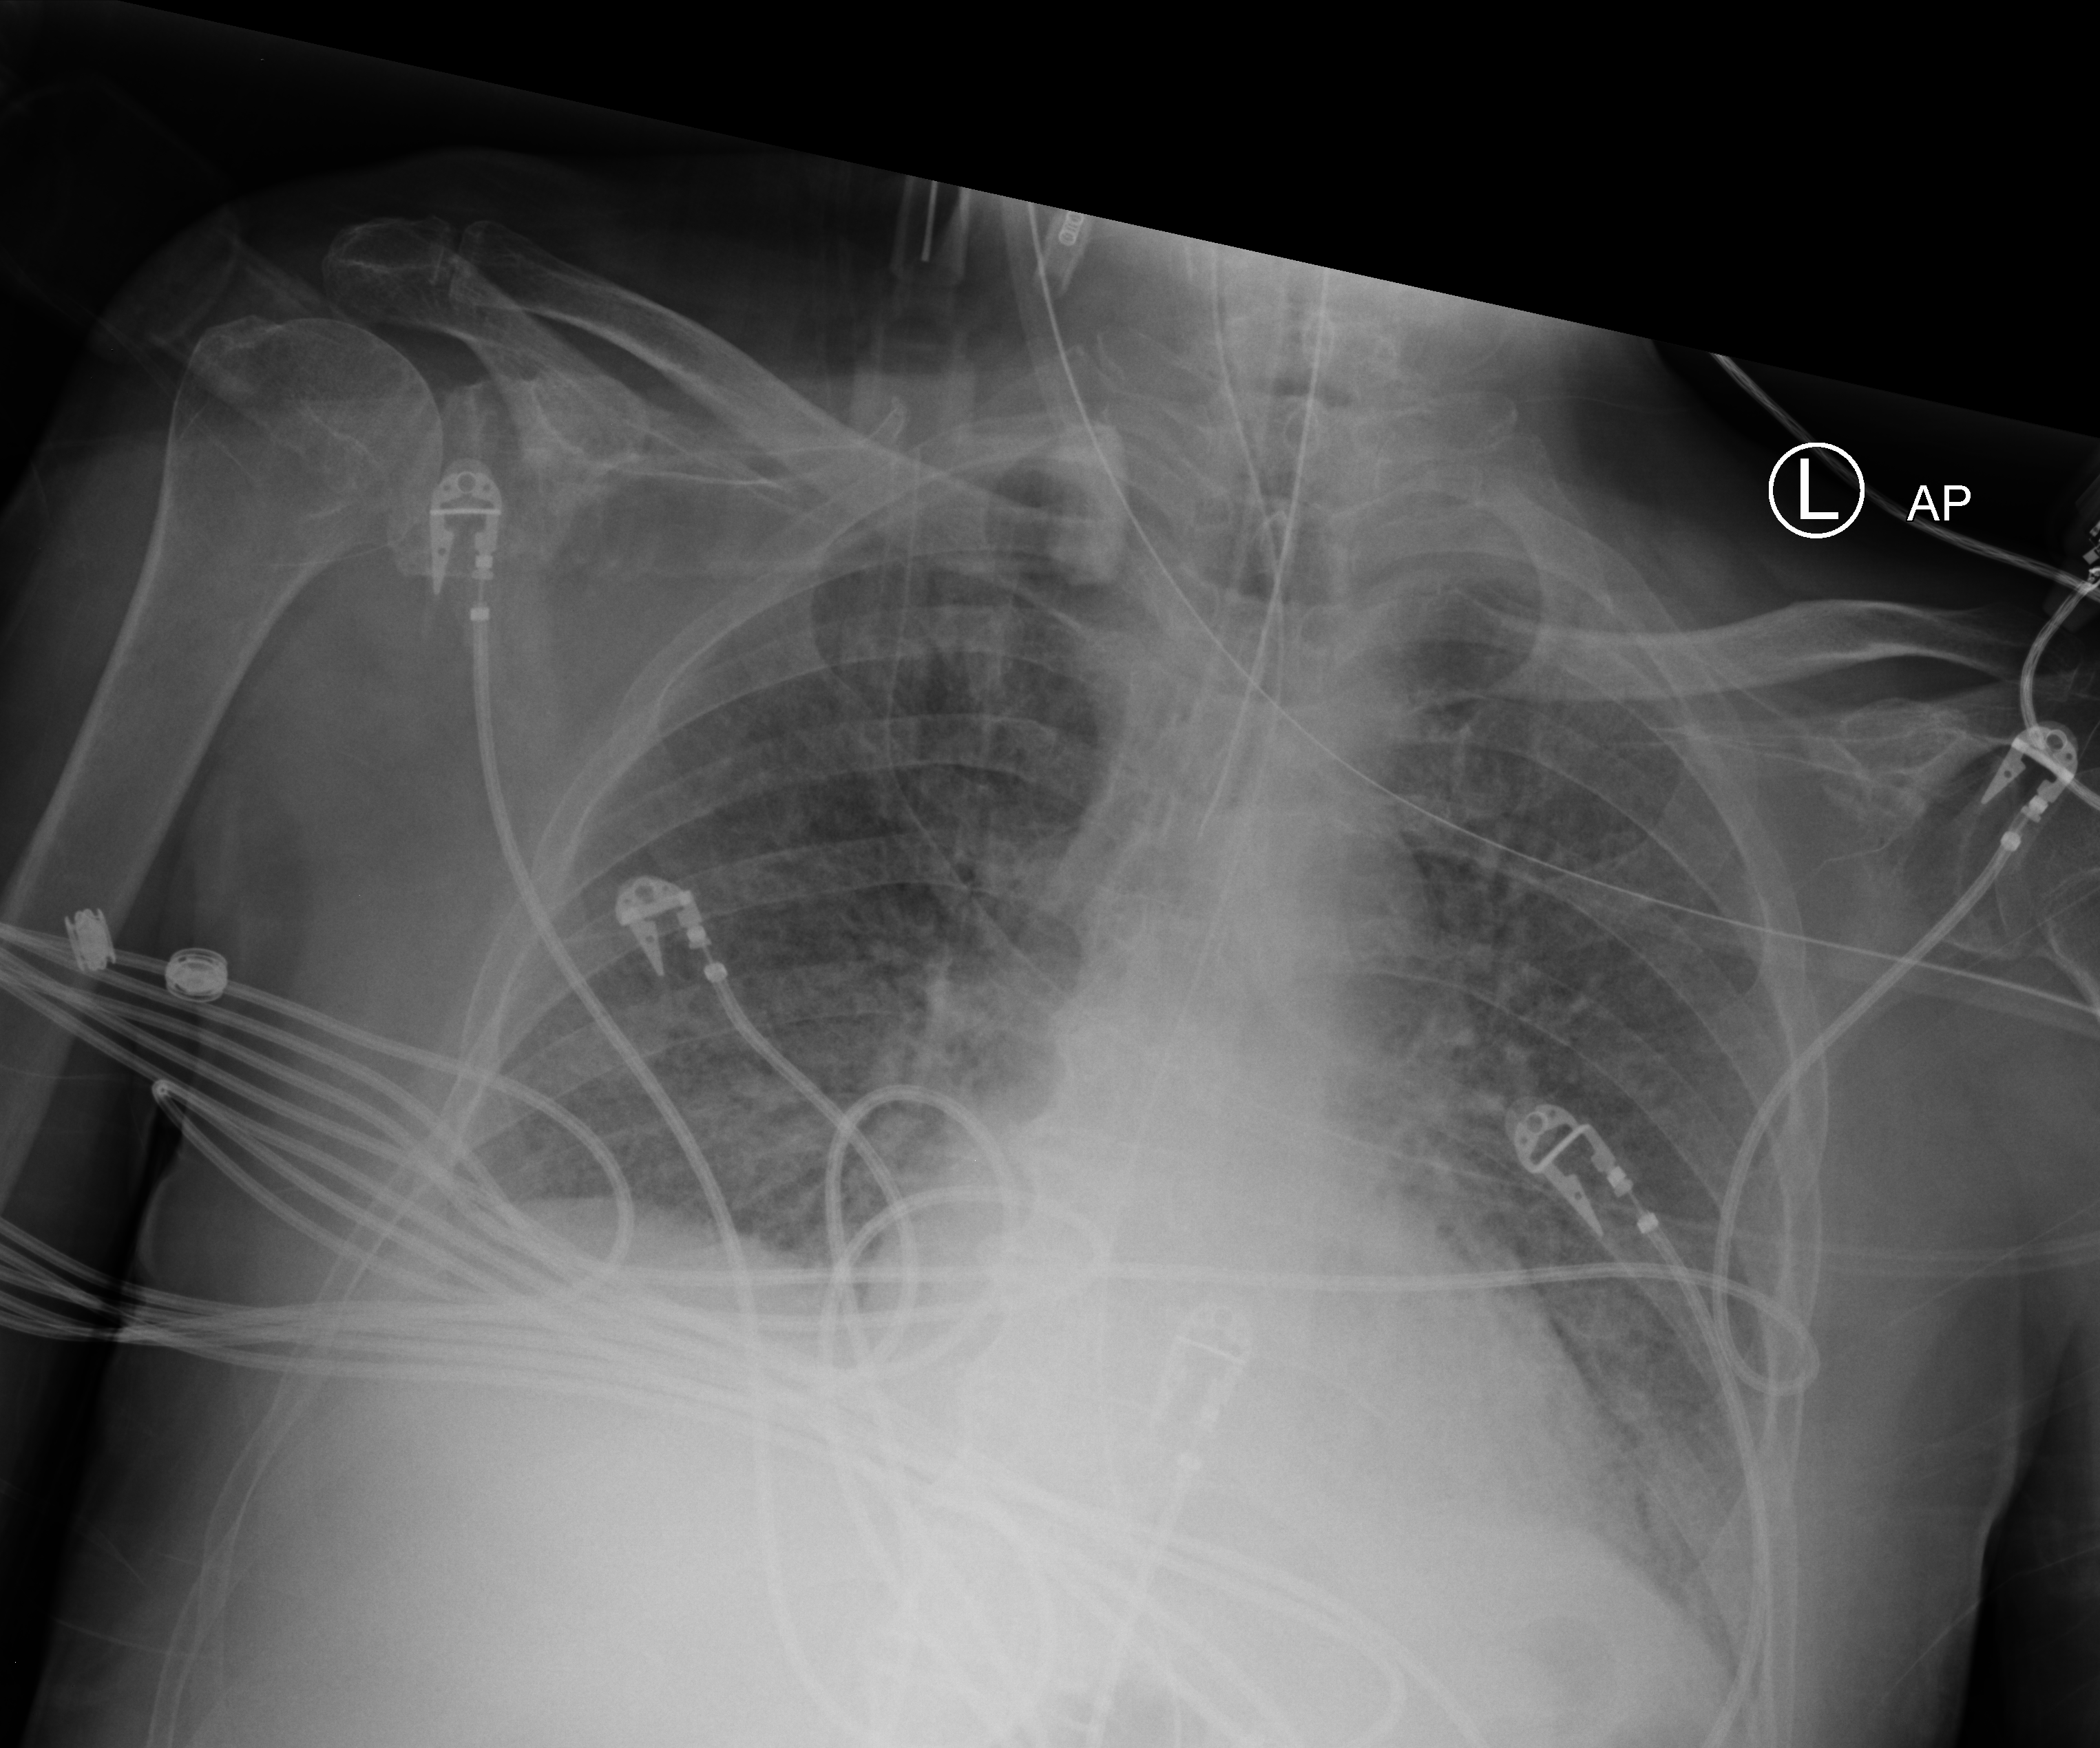
Bedside chest radiograph (computed radiography); anteroposterior (AP) projection. Patient hospitalised with COVID-19; male, aged 75–90 years.
From the hospital-stay record, not from the radiograph (when in the stay this image was taken is not recorded): mechanically ventilated during this hospital stay: yes; diabetes (admission record): no.